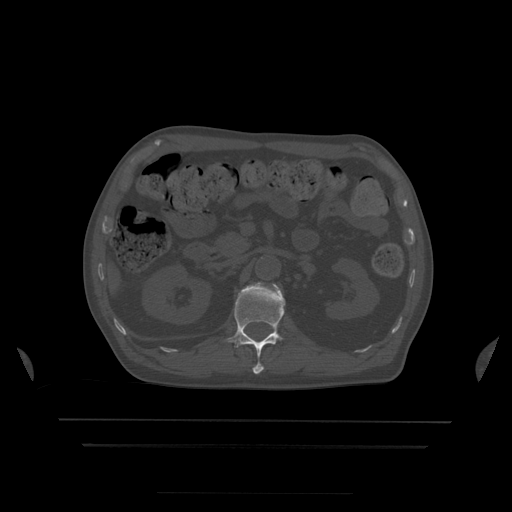
CT including the spine, one axial slice; position 169 of 522 along the scan axis; bone window (W 1800 / L 400 HU); 1.25 mm slice thickness; 512 × 512 image matrix, field of view 436 × 436 mm. Patient age 68 years. From the clinical record (not read from this slice): primary cancer: urothelial.
Annotated regions visible in this slice (semi-automatically segmented with operator editing):
- L1 vertebra: box from (x=227, y=282) to (x=286, y=375) px